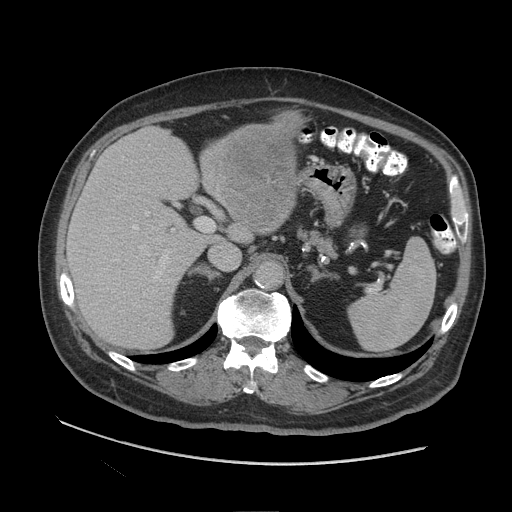
Contrast-enhanced abdominal CT (liver protocol), one axial slice. Slice 57 of 109 in the series (ordered by position). Reconstruction kernel STANDARD. Soft-tissue window (W 400 / L 40 HU). 512 × 512 image matrix, field of view 420 × 420 mm. From the clinical record (not read from this slice): diagnosis: hepatocellular carcinoma (patient treated with transarterial chemoembolisation; whether this scan precedes or follows treatment is not stated here); TNM stage (as recorded): Stage-I; Child-Pugh class: A; tumour nodularity: uninodular.
Annotated regions visible in this slice (semi-automatic segmentation, software-assisted and operator-edited):
- liver parenchyma outside the tumour (the mass and vessels are separate outlines, so this box may not span the whole liver): bounding box [x1, y1, x2, y2] px = [66, 118, 294, 348]
- mass: [216, 122, 295, 232]
- liver vessels: [72, 212, 170, 292]